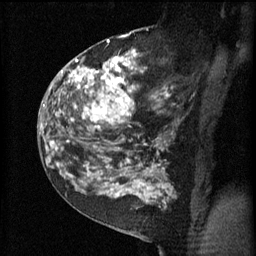
Breast MRI (dynamic contrast-enhanced), one sagittal slice. Slice 32 of 60 in the series (ordered by position). 3 images stored at this slice position (order not interpretable as contrast timing). 1.5 T. TE 4.2 ms, TR 11 ms. 2 mm slice thickness. 256 × 256 image matrix, field of view 180 × 180 mm. Patient: female, 52 years.
Outlined on this slice (semi-automatically segmented with operator editing):
- analysis volume of interest (the breast-tissue region the enhancement analysis was run in; not a lesion): bounding box <81,52,174,157> (left, top, right, bottom; pixels)
- tumour enhancement mask (voxels above the 70 % enhancement threshold inside the analysis volume of interest): <81,52,157,129>